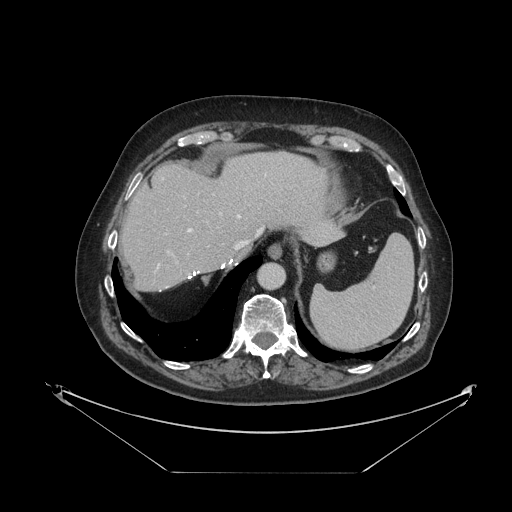
Contrast-enhanced abdominal CT, one axial slice; position 92 of 121 along the scan axis; reconstruction kernel STANDARD; 120 kVp; intravenous contrast given; soft-tissue window (W 400 / L 40 HU); 2.5 mm slice thickness; 512 × 512 image matrix, field of view 500 × 500 mm. Male patient, age 68 years. From the clinical record (not read from this slice): diagnosis: colorectal cancer liver metastases, imaged before liver resection; multiple liver metastases: no; largest metastasis: 4 cm; disease in both lobes: no.
Annotated regions visible in this slice (expert manual segmentation):
- hepatic veins: bounding box <157,215,263,269> (left, top, right, bottom; pixels)
- liver: <122,151,340,291>
- planned liver remnant (the part of the liver to remain after resection): <122,152,340,291>
- portal vein (with intrahepatic branches): <168,213,222,264>